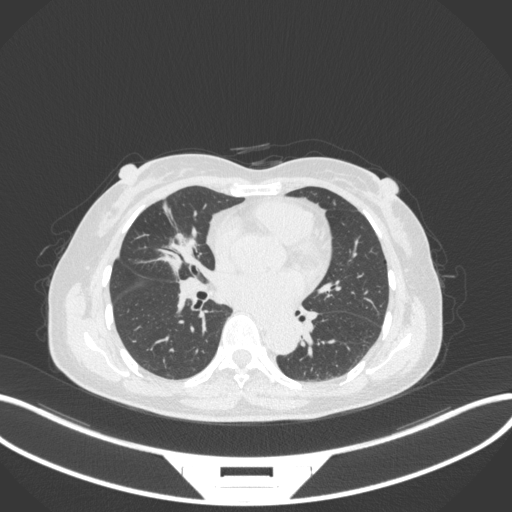
Chest CT, one axial slice. Slice 144 of 282 in the series (ordered by position). Reconstruction kernel B31f. 120 kVp. Lung window (W 1500 / L -600 HU). 1 mm slice thickness. 512 × 512 image matrix, field of view 400 × 400 mm. Female patient, age 51 years. Case-level facts recorded for this patient, not image findings: clinical TNM (as recorded): T1c N0 M0; histopathological grade: G2.
Structures marked on this image (bounding box drawn by a radiologist):
- lung tumour (recorded histology: adenocarcinoma): bounding box [x1, y1, x2, y2] px = [155, 228, 198, 276]